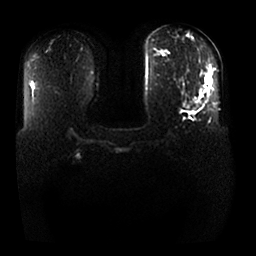
Breast MRI, one axial slice. Position 12 of 25 along the scan axis. Diffusion-weighted series; image 2 of 4 stored at this slice position (different b-values; order by instance number). 1.5 T. 4 mm slice thickness. 256 × 256 image matrix. Female patient.
Structures marked on this image (expert manual segmentation):
- tumour on diffusion-weighted imaging: box from (x=184, y=104) to (x=189, y=109) px